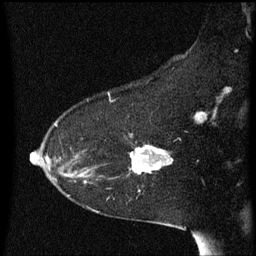
Breast MRI (dynamic contrast-enhanced), one sagittal slice. Position 41 of 60 along the scan axis. Dynamic contrast-enhanced series, image 2 of 3 at this slice position (ordered by acquisition). 1.5 T. TE 4.2 ms, TR 8.4 ms. 256 × 256 image matrix, field of view 200 × 200 mm. Female patient, age 54 years. From the clinical record (not read from this slice): setting: breast cancer imaged before/during neoadjuvant chemotherapy; receptor status: HR-positive, HER2-negative.
Outlined on this slice (semi-automatic segmentation, software-assisted and operator-edited):
- analysis volume of interest (the breast-tissue region the enhancement analysis was run in; not a lesion): box from (x=117, y=136) to (x=175, y=179) px
- tumour enhancement mask (voxels above the 70 % enhancement threshold inside the analysis volume of interest): (x=132, y=146)–(x=173, y=173)